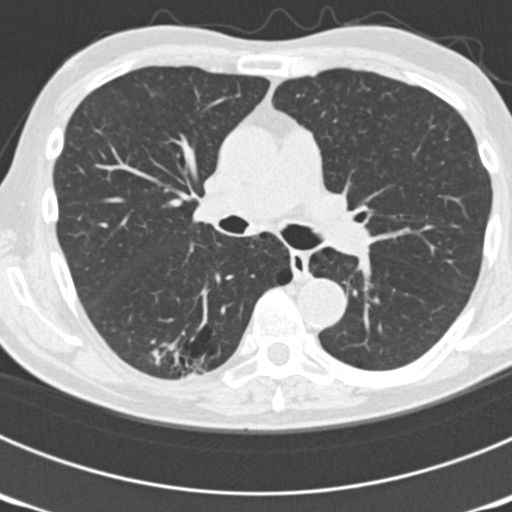
Low-dose screening chest CT, axial slice; third annual screen; lung window (W 1500 / L -600 HU); standard (soft-tissue) reconstruction kernel (B30f); 120 kVp. Male, age 70 years at enrolment. Current smoker at enrolment.
Expert-annotated lung lesion, bounding box <143,310,236,385> (left, top, right, bottom; pixels). The screening reader recorded 3 non-calcified nodules or masses ≥4 mm on this exam; which of them this box marks is not recorded. Participant outcome: lung cancer diagnosed 14 days after this screen — bronchiolo-alveolar adenocarcinoma, NOS, right lower lobe, poorly differentiated (G3), stage IB (AJCC 6th edition), 30 mm at pathology.